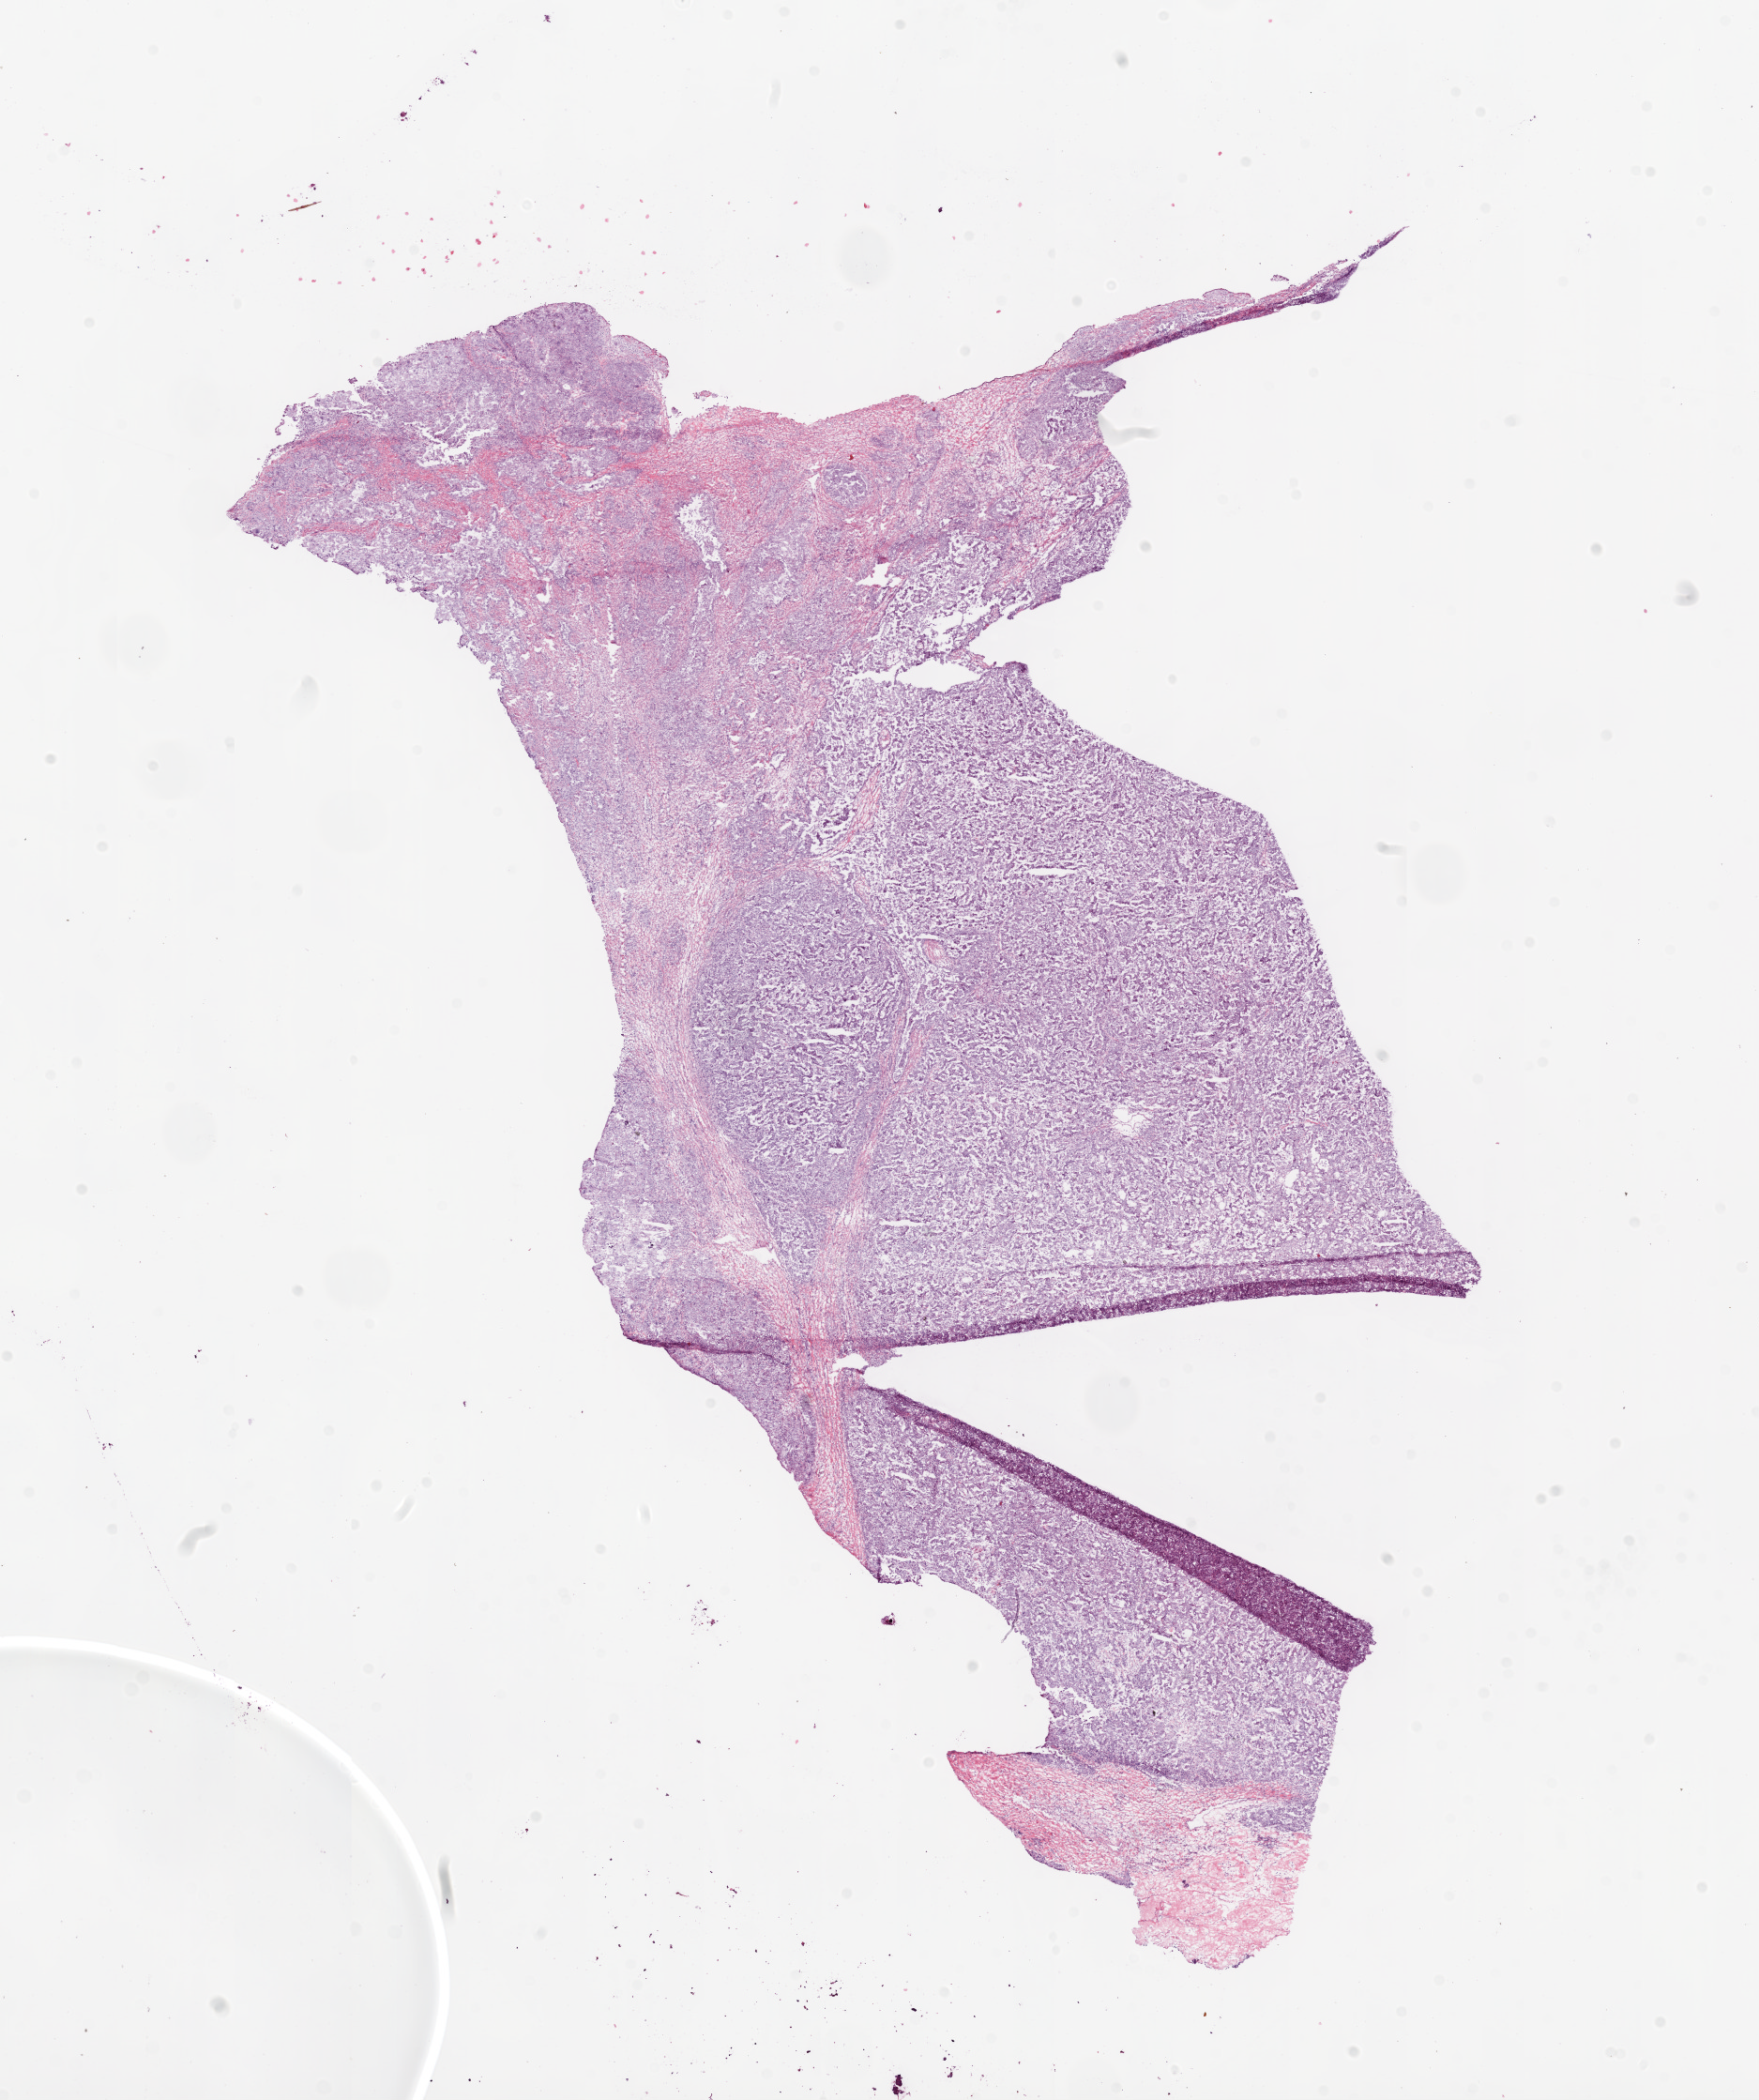
Hematoxylin and eosin (H&E) stained whole-slide image, whole scanned area (about 15.0 x 18.0 mm) shown as a low-resolution overview. Frozen section from the bottom of the tissue portion. Ovary, primary tumour sample. Female patient; age at initial diagnosis 75 years. Histologic grade: G3 (poorly differentiated). Composition of this section per pathologist review: tumour cells 85%, tumour nuclei 85%, normal cells 0%, stromal cells 15%, necrosis 0%.
* FIGO stage: IV
* diagnosis: Serous cystadenocarcinoma, NOS